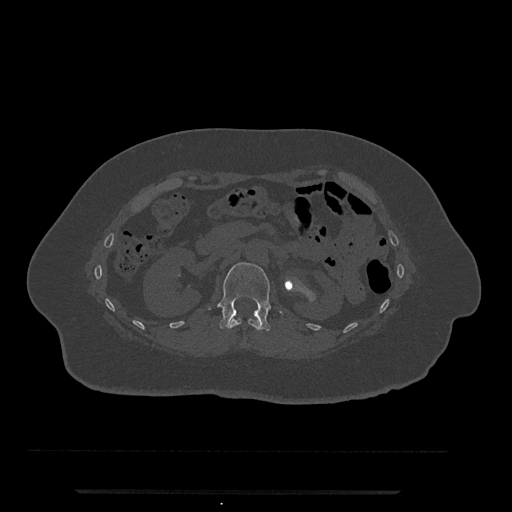
CT including the spine, one axial slice. Position 120 of 797 along the scan axis. Reconstruction kernel Br40s/3. Bone window (W 1800 / L 400 HU). 512 × 512 image matrix. Female patient, age 51 years. Case-level facts recorded for this patient, not image findings: primary cancer: neuro; vertebrae with lytic lesions (as recorded): T8.
Outlined on this slice (semi-automatic segmentation, software-assisted and operator-edited):
- L1 vertebra: bounding box (x1, y1, x2, y2) in pixels: (218, 262, 270, 331)
- T12 vertebra: (227, 318, 262, 331)